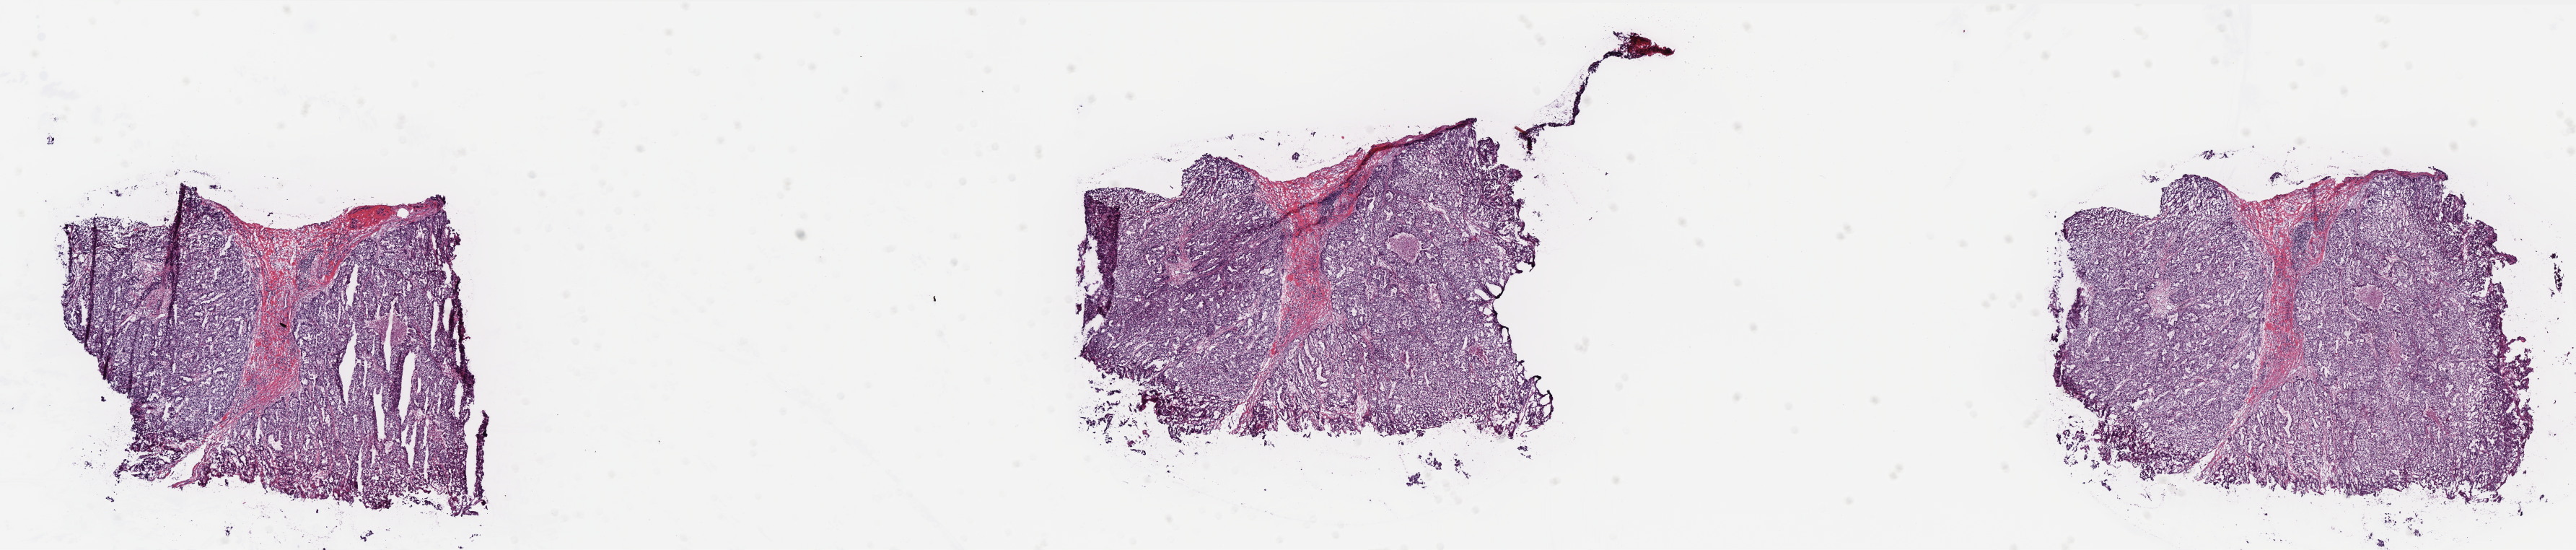
H&E whole-slide image — shown as a low-resolution overview of the whole scanned area (about 28.6 x 6.1 mm); frozen section; breast, primary tumour sample. Female, age 41 years at initial diagnosis. Composition of this section per pathologist review: tumour cells 80%, tumour nuclei 80%, normal cells 0%, stromal cells 10%, necrosis 10%. Infiltration values recorded for this section: lymphocyte infiltration 10%, monocyte infiltration 10%, neutrophil infiltration 25%.
Lymph nodes positive (case pathology): 0 of 5 examined. Histologic diagnosis: Infiltrating duct carcinoma, NOS. AJCC pathologic stage: IIIB. TNM: T4 N0 M0.